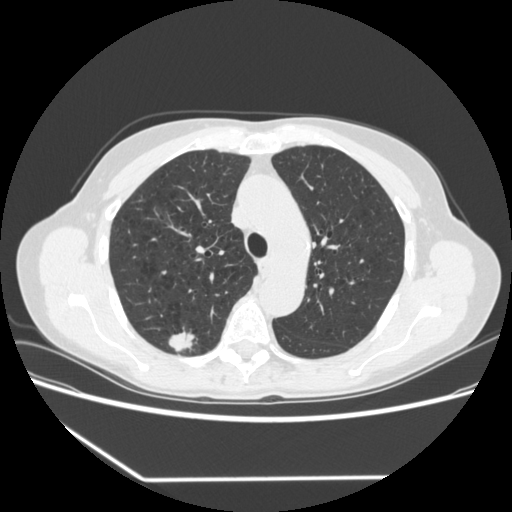
Axial slice from a low-dose chest CT screening exam, baseline annual screen, lung window (W 1500 / L -600 HU), slice 242 of 323 in the series, 512 × 512 image matrix. Female, age 67 years at enrolment.
- Expert reader's lesion annotation, bounding box <156,323,200,359> (left, top, right, bottom; pixels).
- The screening reader recorded 2 non-calcified nodules or masses ≥4 mm on this exam; which of them this box marks is not recorded.
- Lung cancer was diagnosed 29 days after this screen: adenocarcinoma, NOS, right upper lobe, moderately differentiated (G2), stage IA (AJCC 6th edition), 24 mm at pathology.